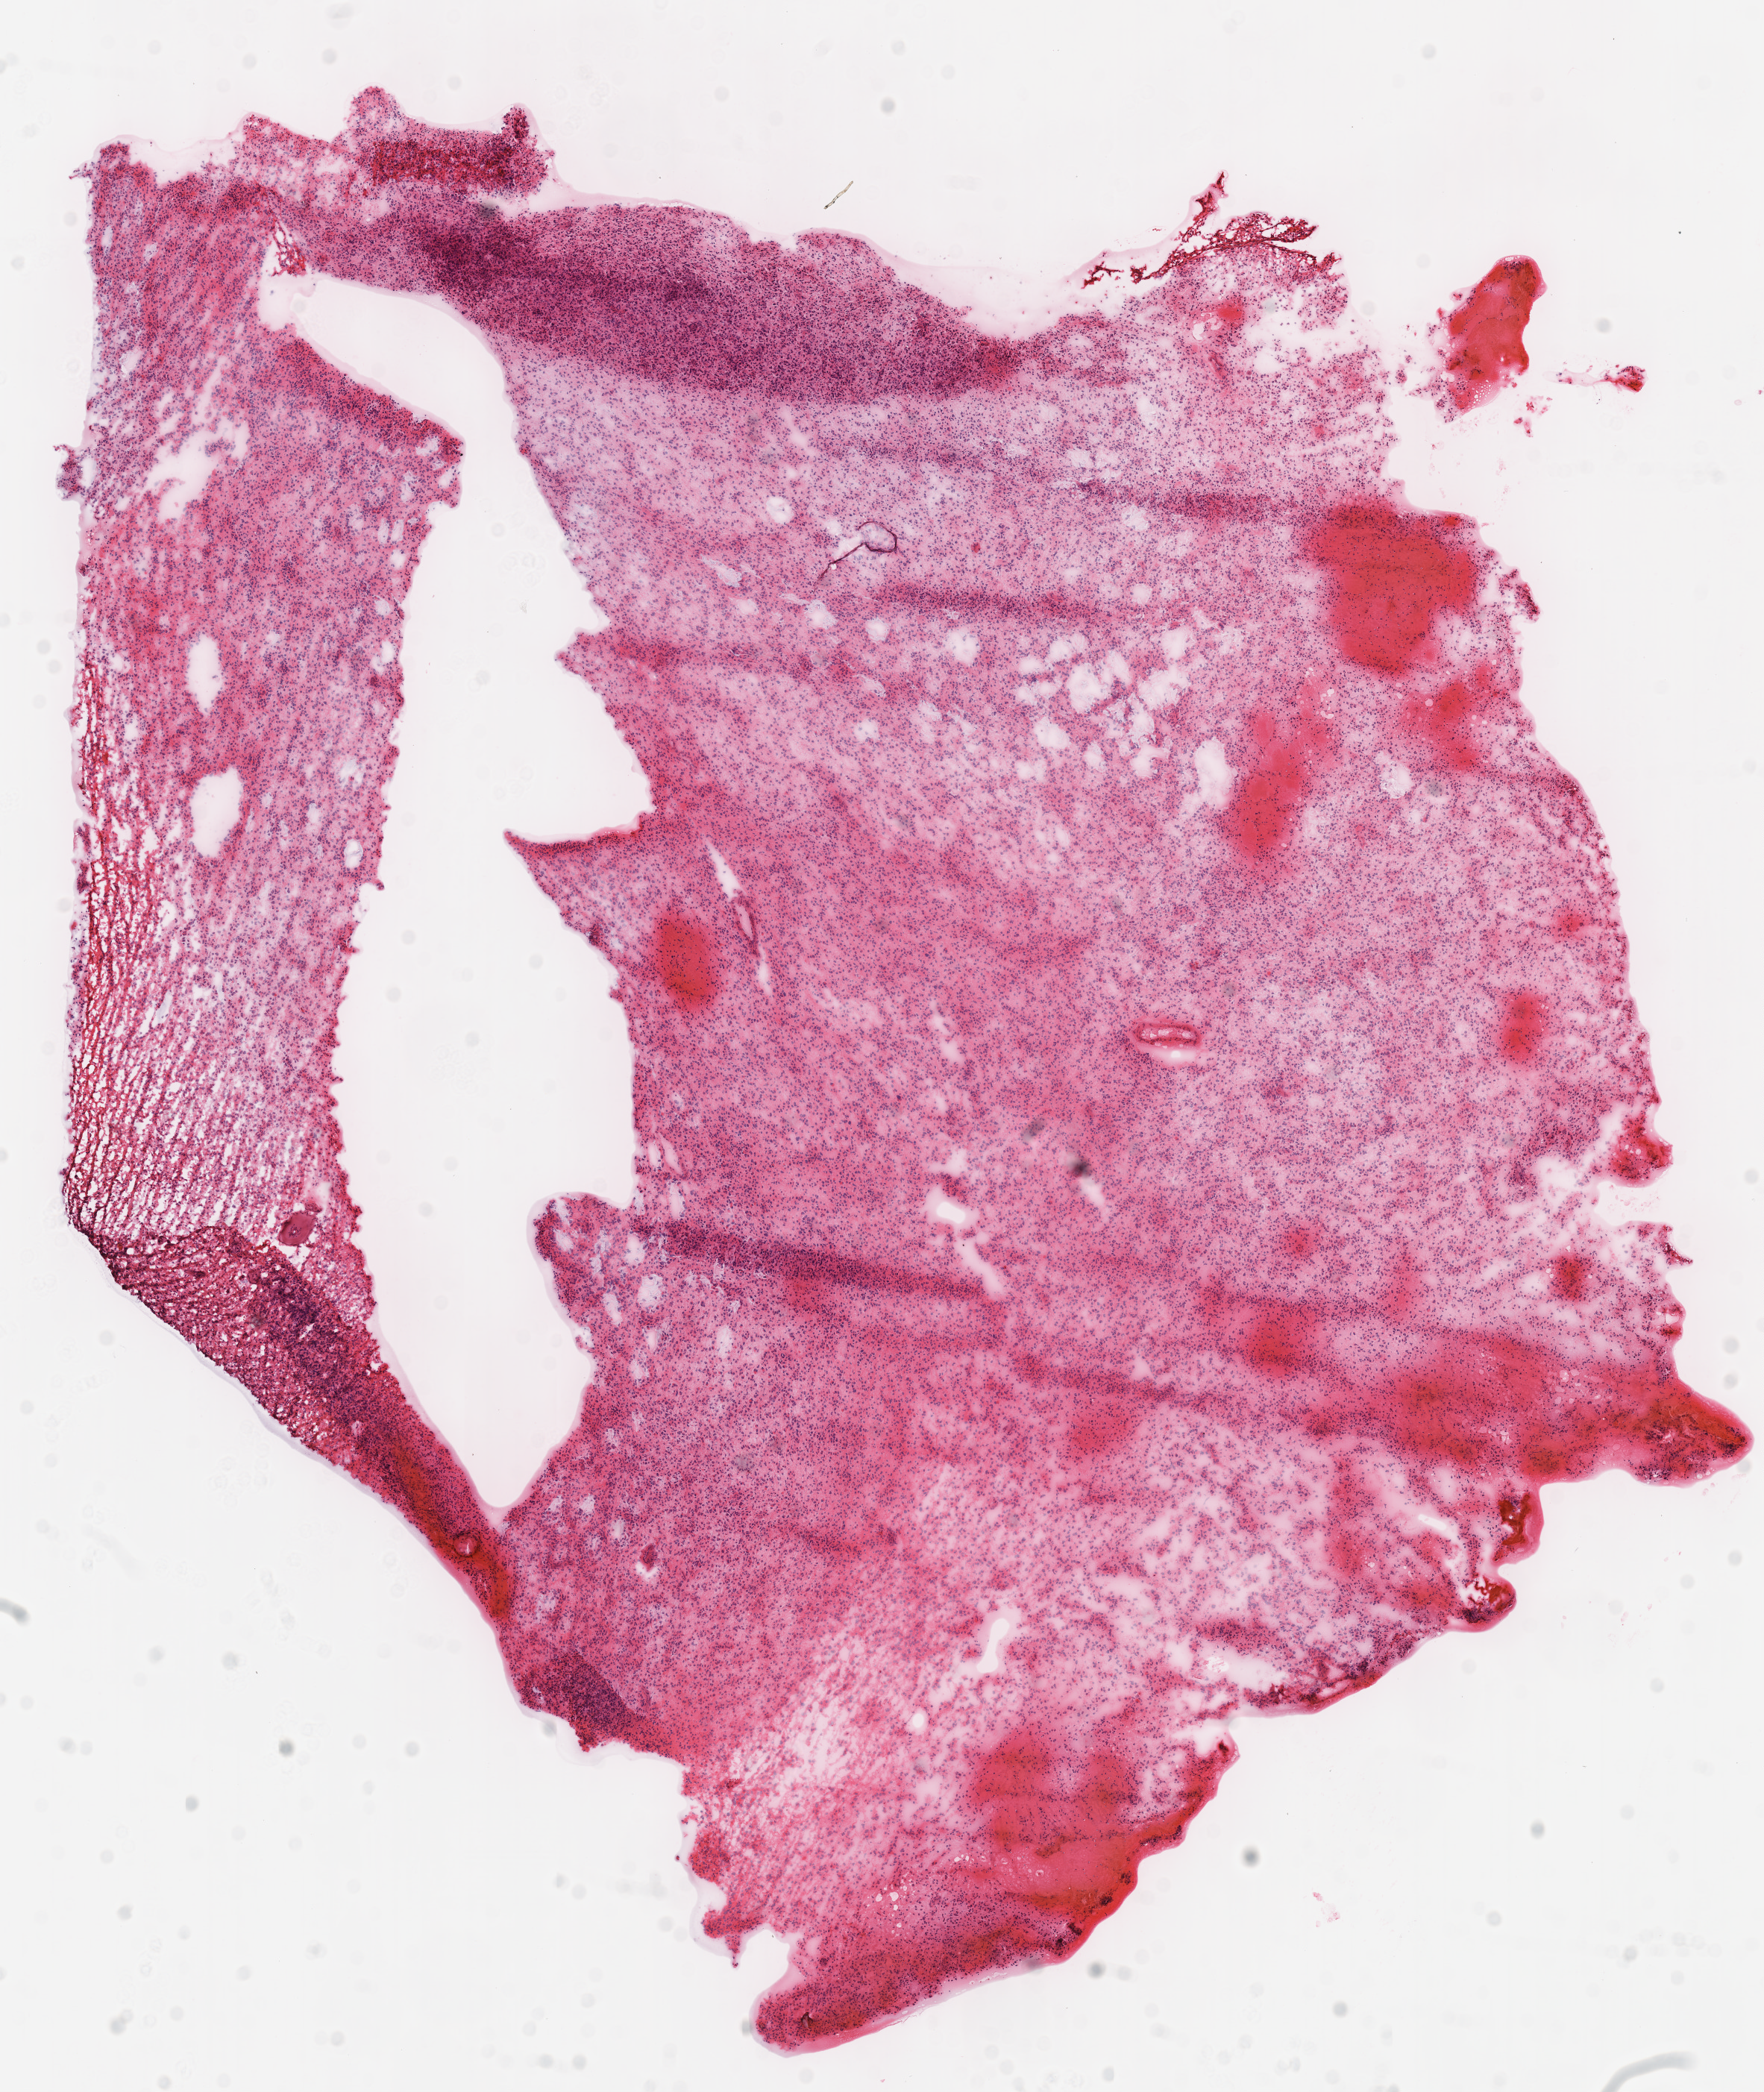
H&E whole-slide image, low-resolution overview of the scanned area, about 9.3 x 11.0 mm (from a 40x scan); frozen section from the top of the tissue portion; sample: primary tumour, brain. Patient: male, age at initial diagnosis 36 years. Histologic grade: G3 (poorly differentiated). Composition of this section per pathologist review: tumour cells 100%, tumour nuclei 80%, normal cells 0%, stromal cells 0%, necrosis 0%.
* laterality: right
* diagnosis: Astrocytoma, anaplastic (cerebrum)